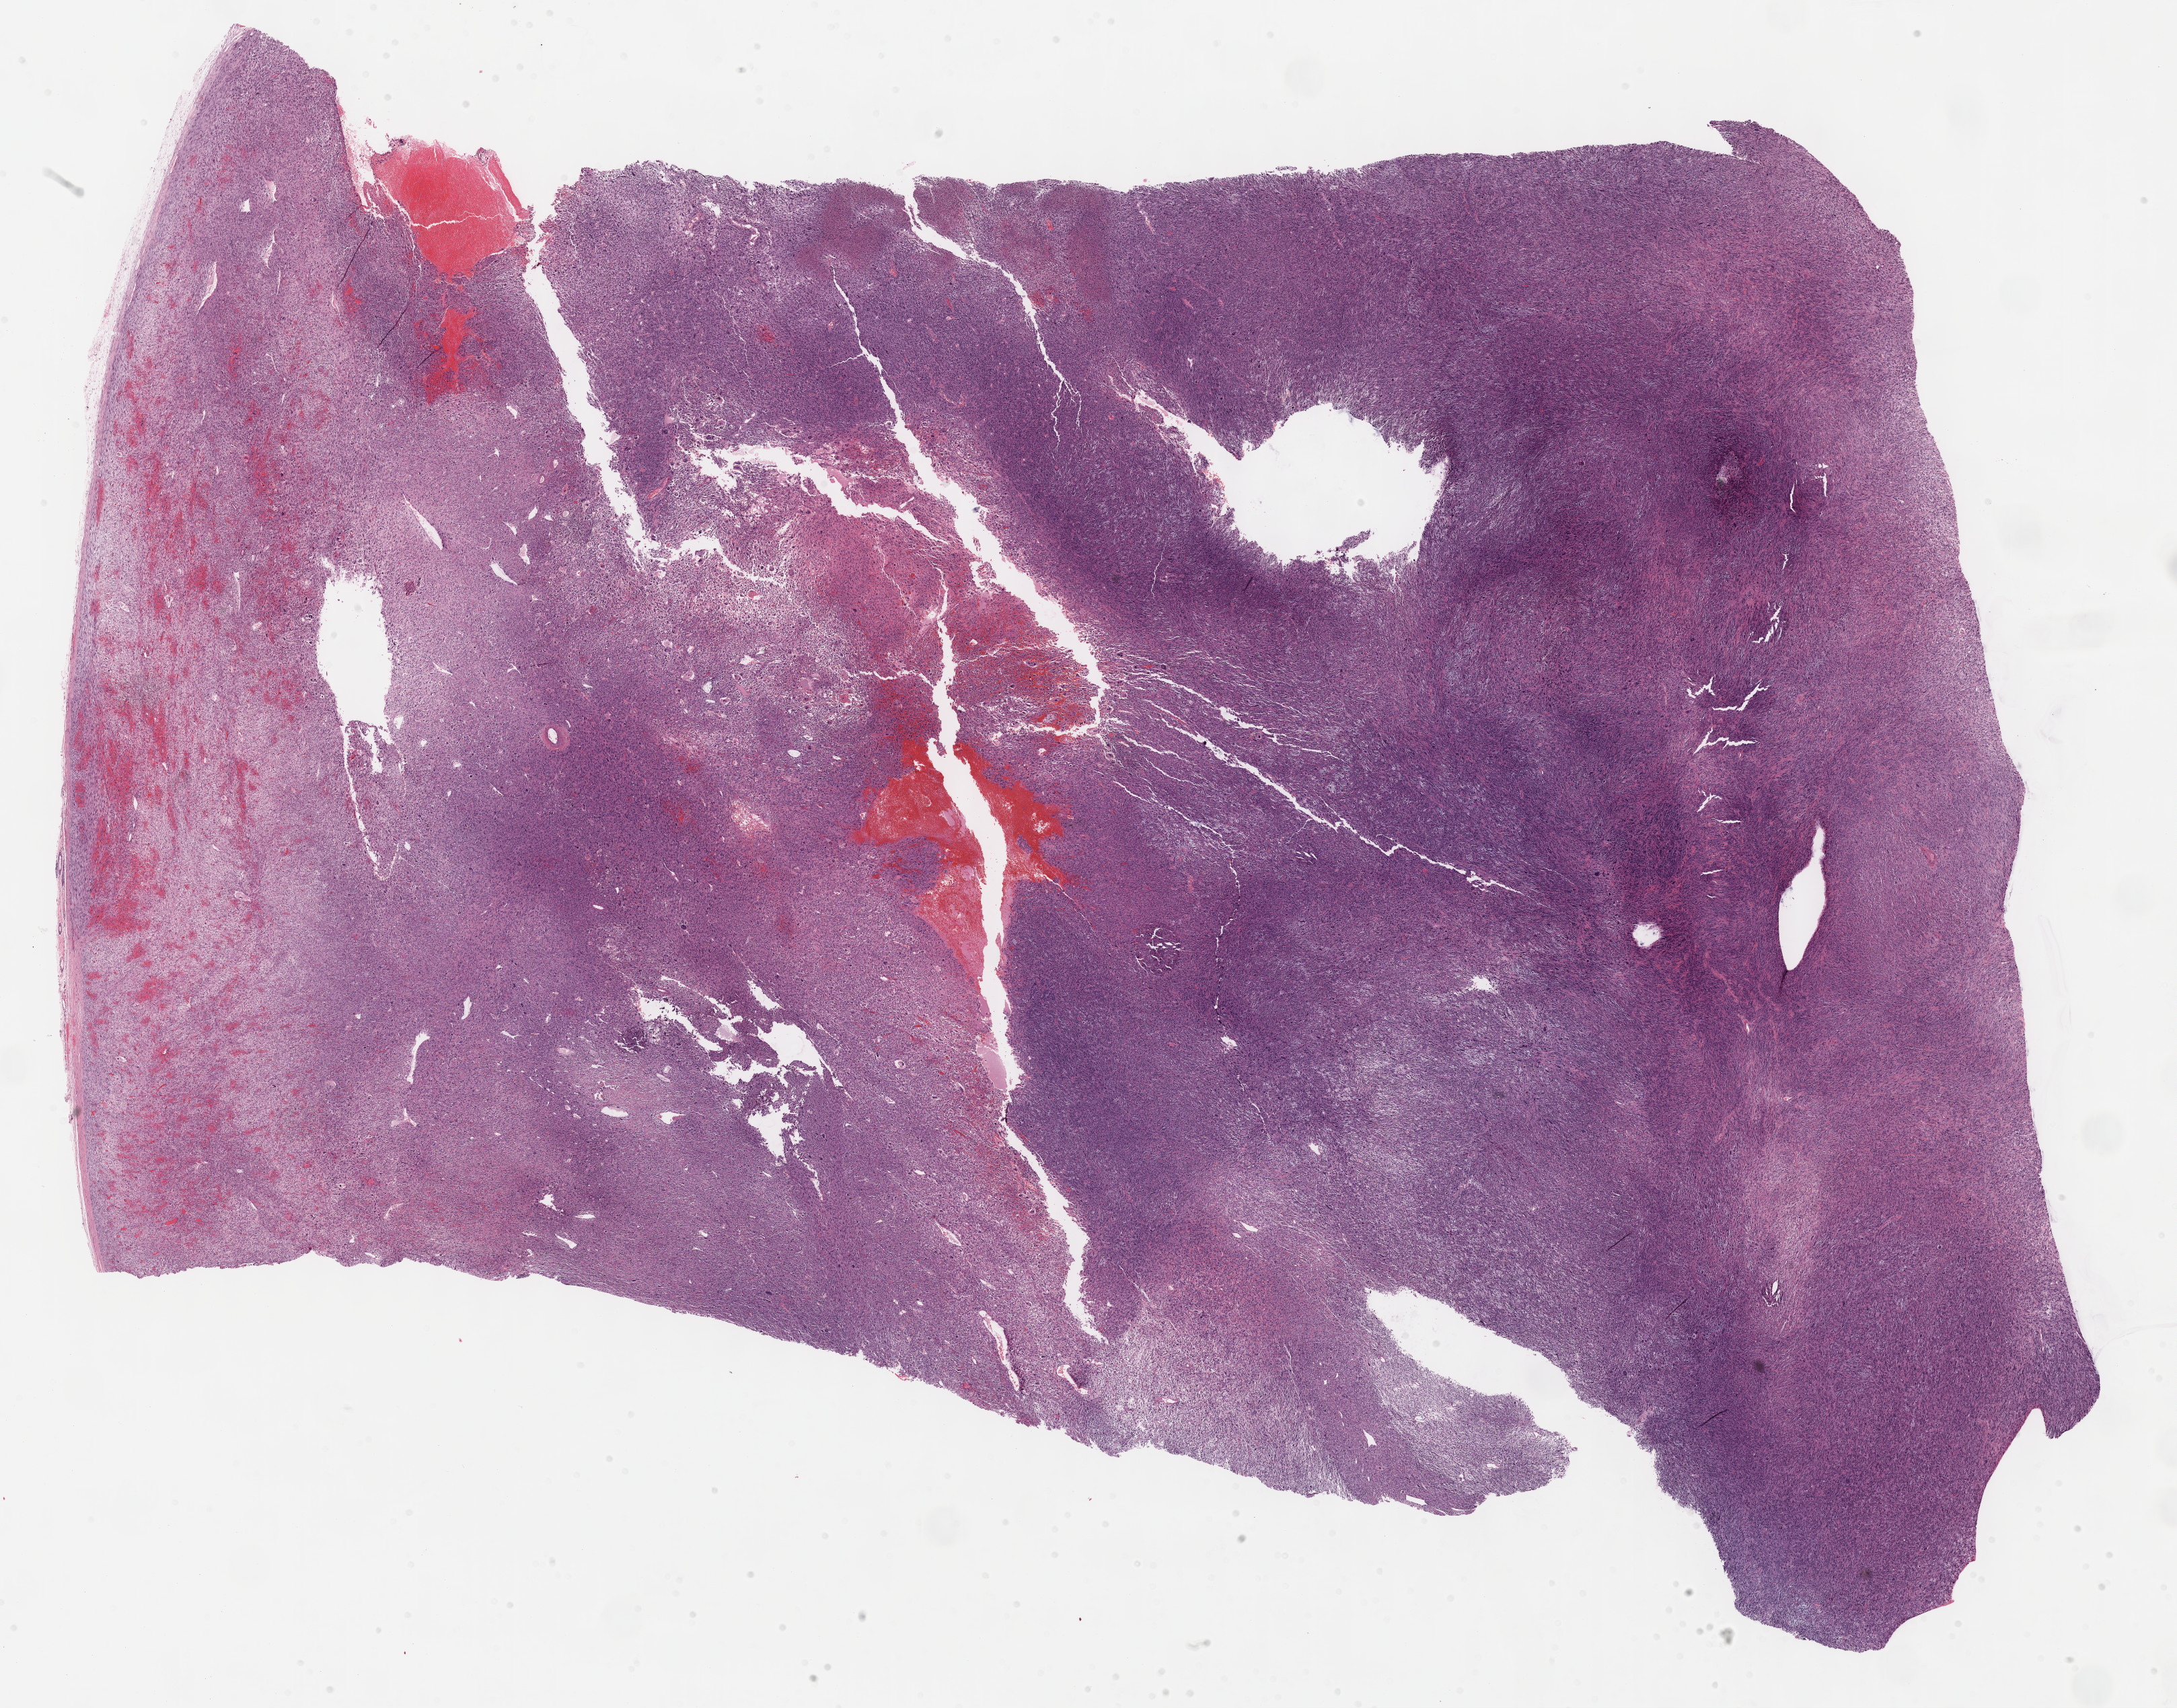
Whole-slide histology image, H&E — a low-resolution overview of the entire scanned area, about 26.2 x 20.5 mm (slide scanned at 40x), formalin-fixed paraffin-embedded (FFPE) diagnostic section, sample: primary tumour, connective, subcutaneous and other soft tissues. Male, age 79 years at initial diagnosis.
* diagnosis: Malignant fibrous histiocytoma (connective, subcutaneous and other soft tissues of lower limb and hip)